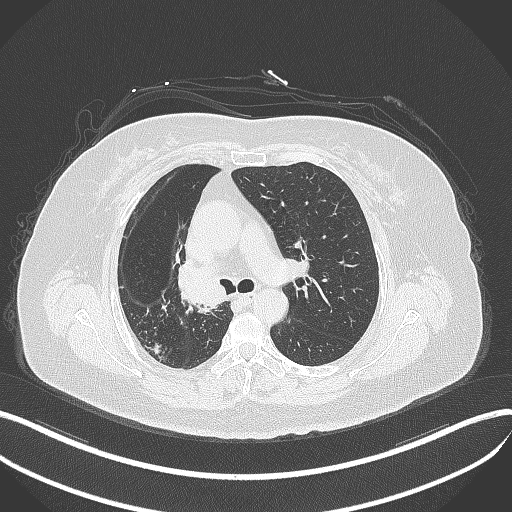
Chest CT, one axial slice. Reconstruction kernel B70f. 120 kVp. Lung window (W 1500 / L -600 HU). 1 mm slice thickness. 512 × 512 image matrix. Female patient, age 60 years. Case-level facts recorded for this patient, not image findings: clinical TNM (as recorded): T1c N0 M0.
Annotated regions visible in this slice (bounding box drawn by a radiologist):
- lung tumour (recorded histology: squamous cell carcinoma): box from (x=173, y=256) to (x=230, y=311) px